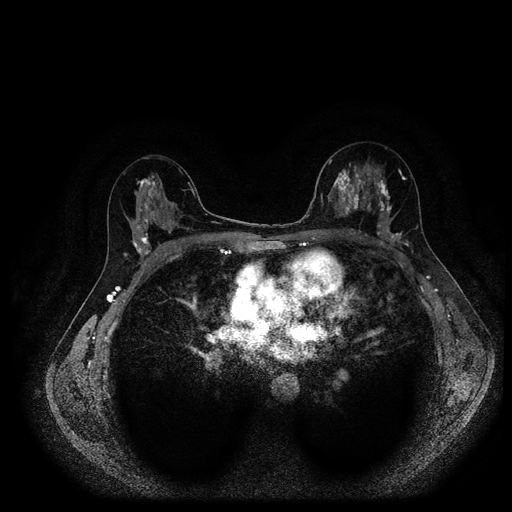
Breast MRI (dynamic contrast-enhanced, multi-phase), one axial slice. Dynamic contrast-enhanced series, time point 2 of 5 at this slice position (early post-contrast). 1.5 T. TE 2.7 ms, TR 5.4 ms. 2 mm slice thickness. 512 × 512 image matrix, field of view 340 × 340 mm. Patient: female, 40 years.
Annotated regions visible in this slice (semi-automatic segmentation, software-assisted and operator-edited):
- breast lesion (labelled 'tumour' in the annotation; benign lesions carry a separate 'benign' label): bounding box (x1, y1, x2, y2) in pixels: (337, 164, 370, 219)